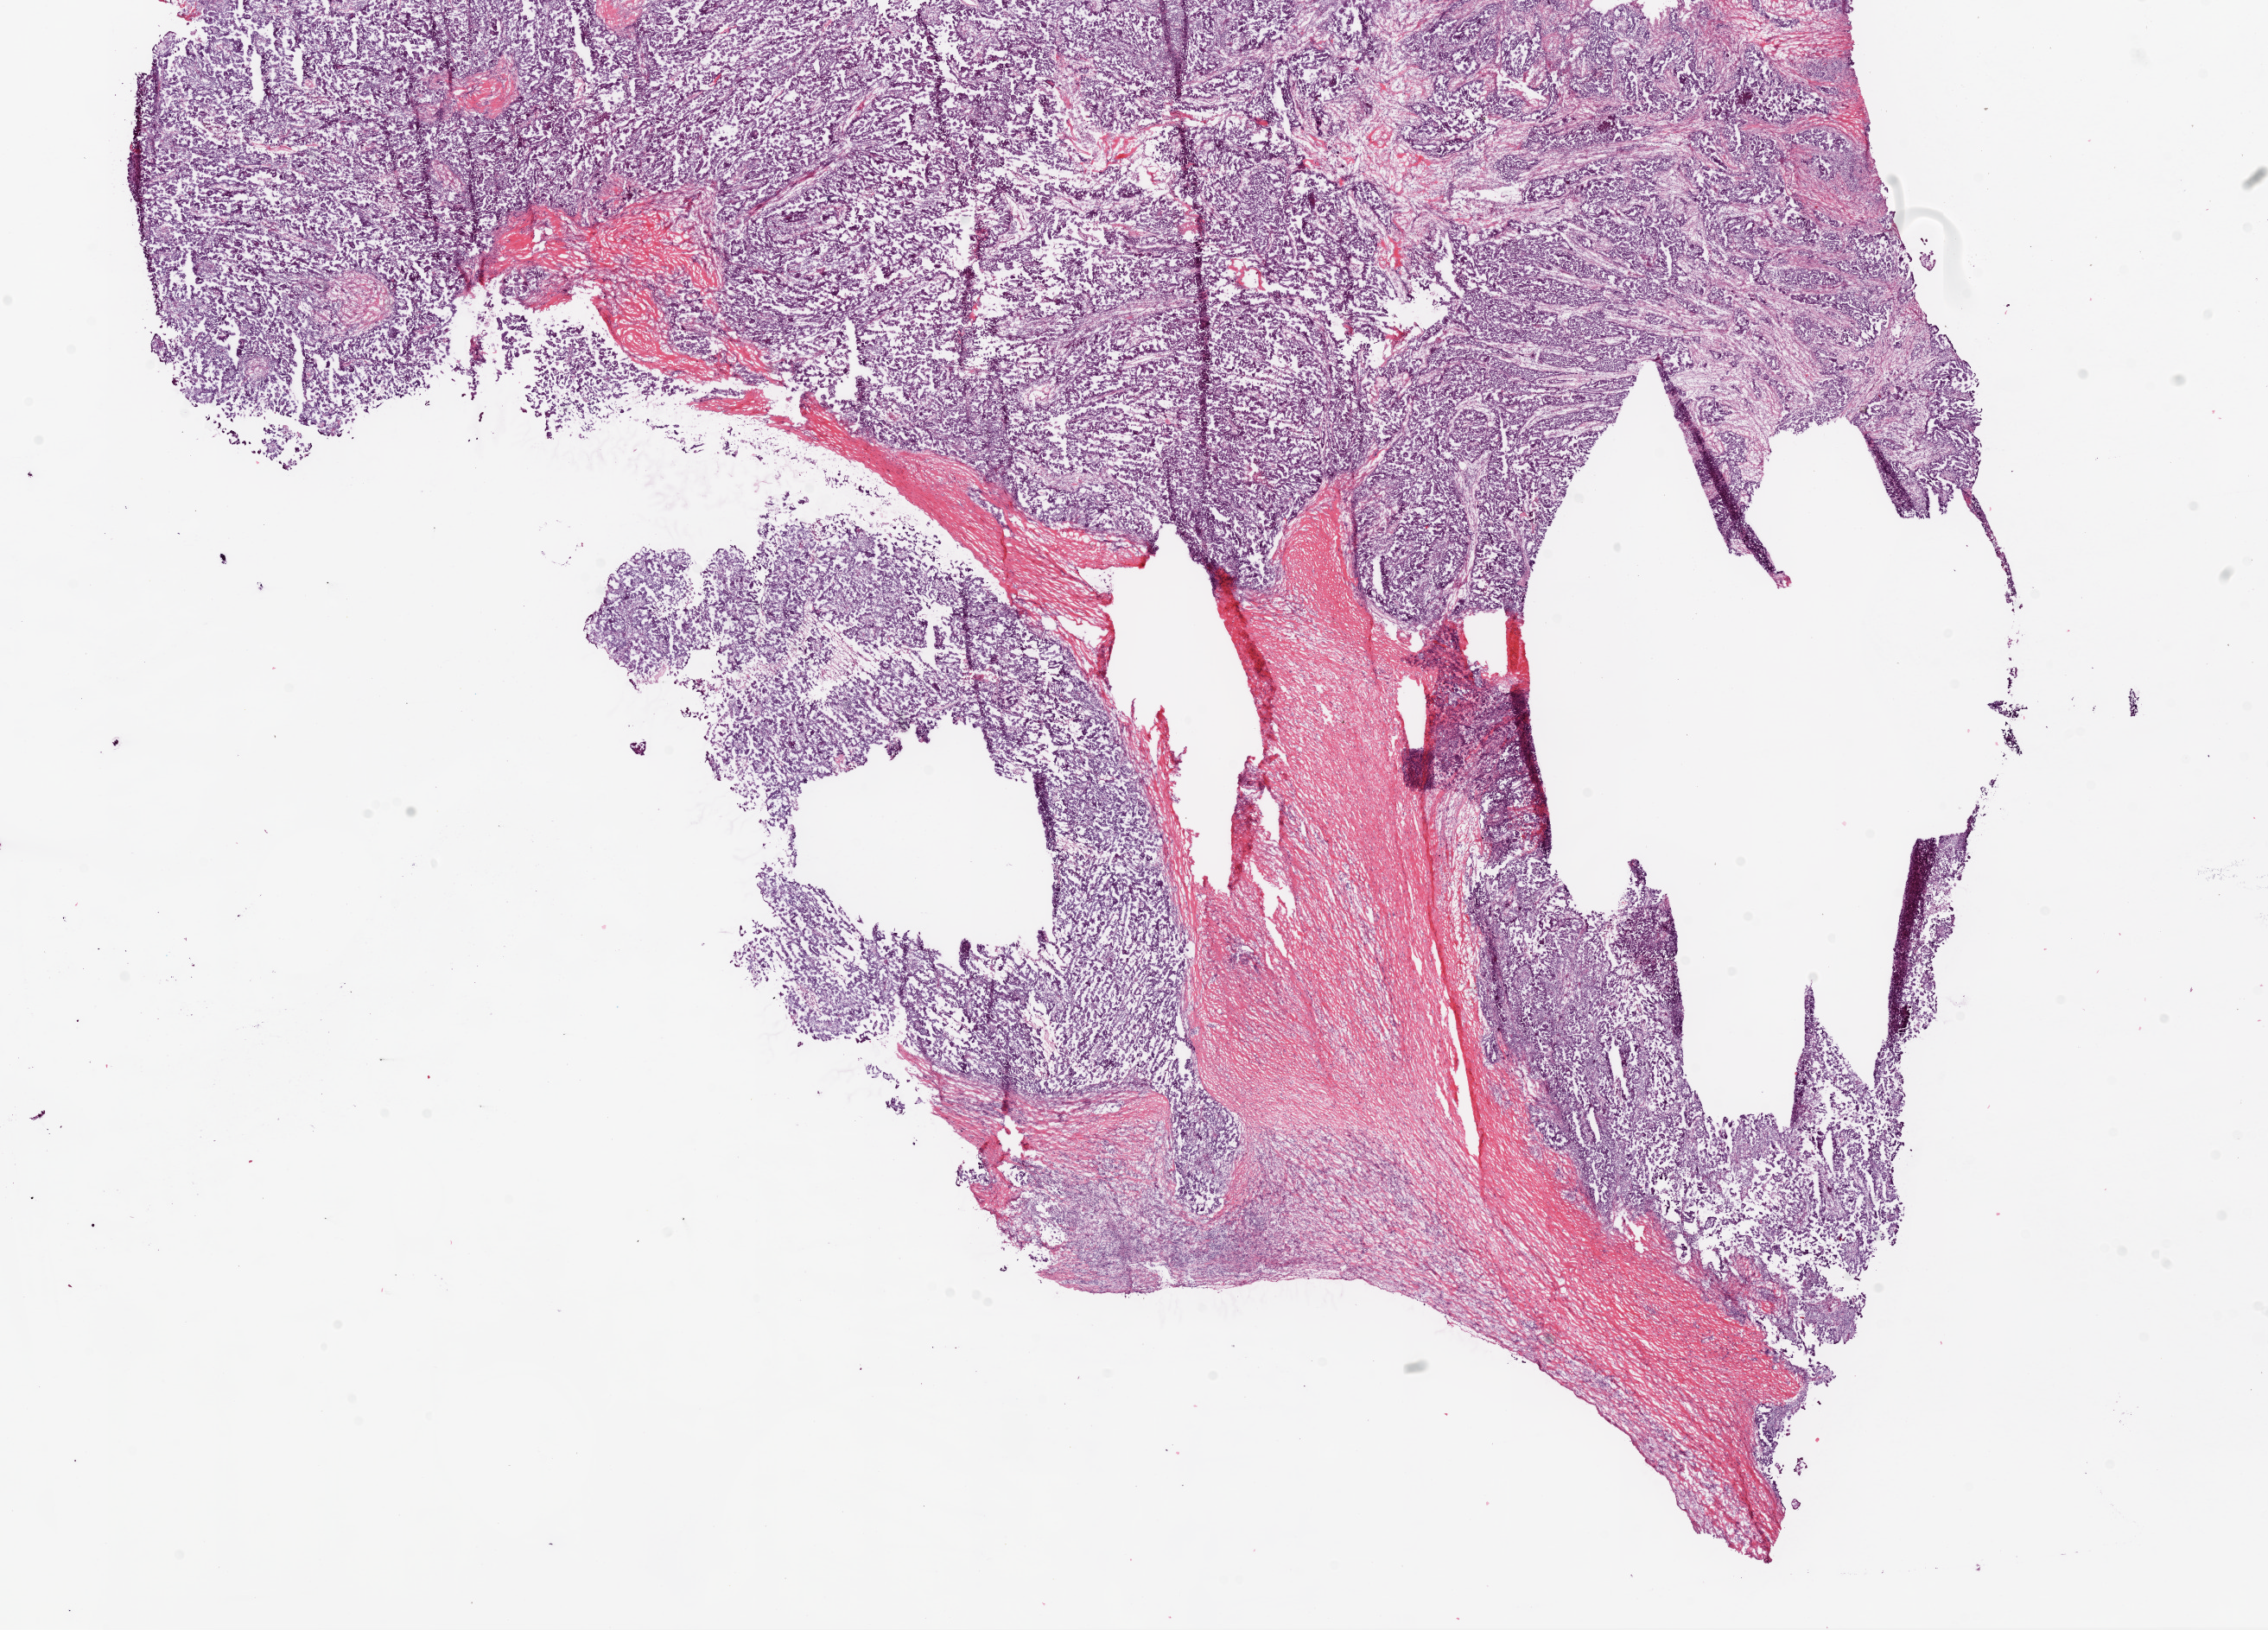
H&E-stained whole-slide image — a low-resolution overview of the entire scanned area, about 21.1 x 15.1 mm (slide scanned at 20x), frozen section, ovary, primary tumour sample. Female patient; age at initial diagnosis 58 years. Slide review estimates, as recorded: tumour cells 80%, tumour nuclei 90%.
Diagnosis: Serous cystadenocarcinoma, NOS.